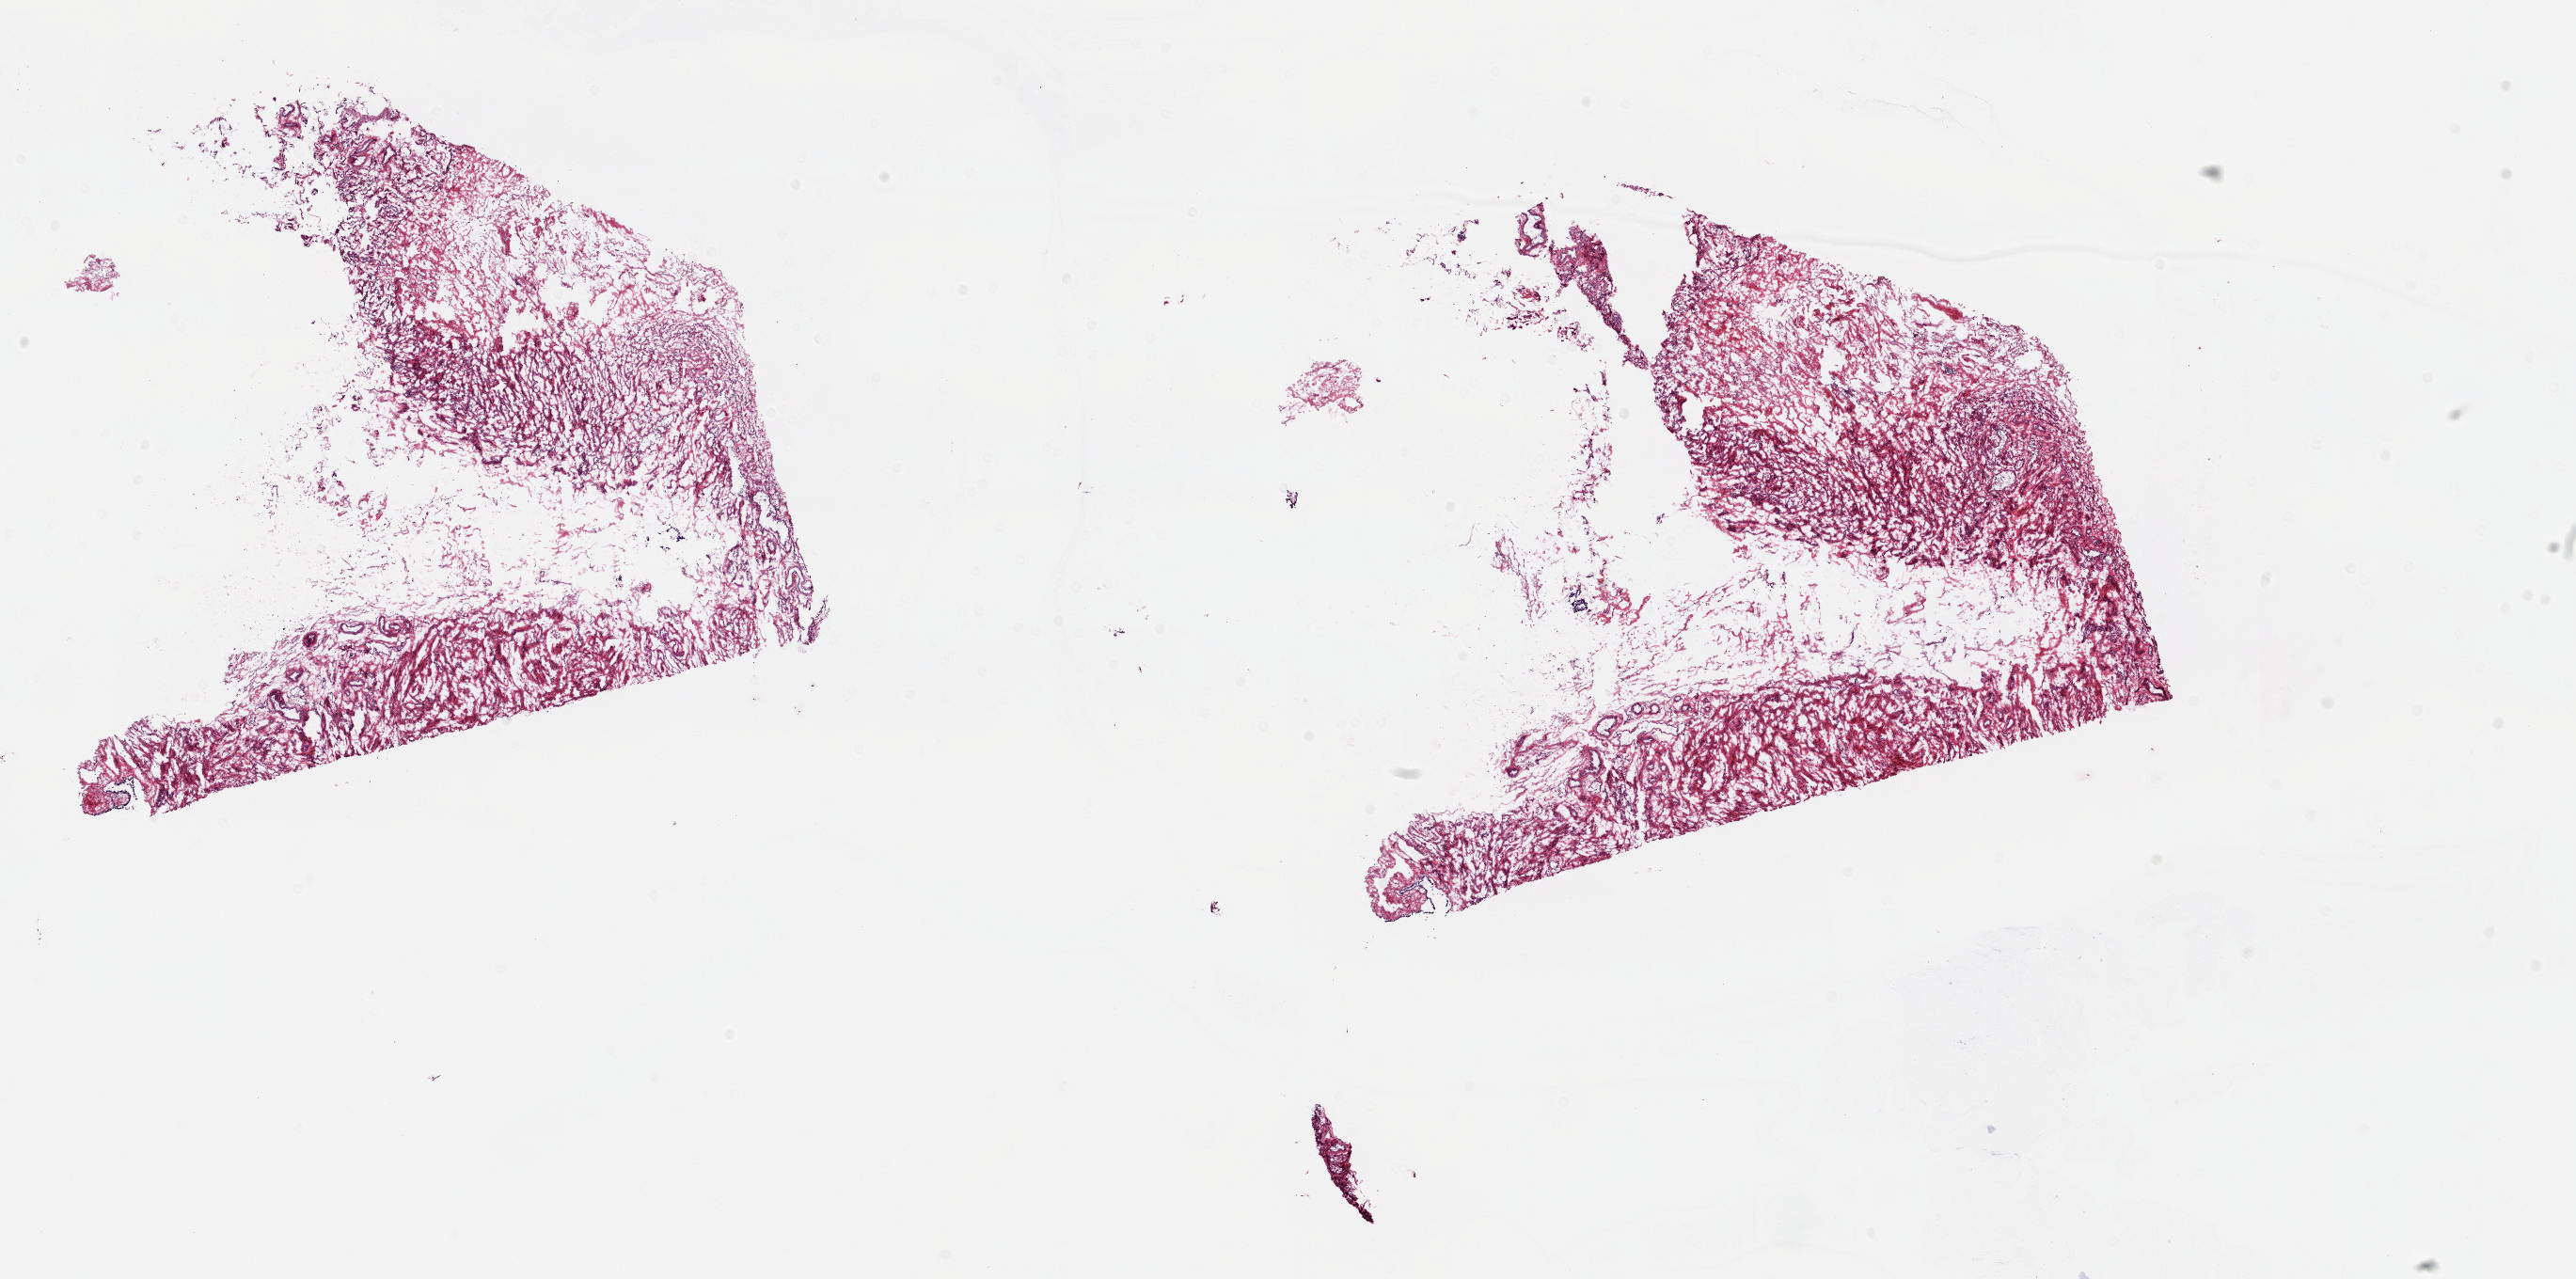
Digitized Hematoxylin and eosin (H&E) stained tissue section (whole slide), a low-resolution overview of the entire scanned area, about 21.8 x 10.8 mm (acquisition: 20x scan). Frozen section from the top of the tissue portion. Sample: solid tissue normal (non-tumour tissue), uterus. Female patient; age at initial diagnosis 60 years. Composition of this section per pathologist review: tumour cells 0%, tumour nuclei 0%, normal cells 100%, stromal cells 0%, necrosis 0%. Infiltration values recorded for this section: lymphocyte infiltration 30%, monocyte infiltration 20%, neutrophil infiltration 30%.
This section: solid tissue normal (non-tumour) sample from the same patient. Patient diagnosis: Endometrioid adenocarcinoma, NOS (endometrium).